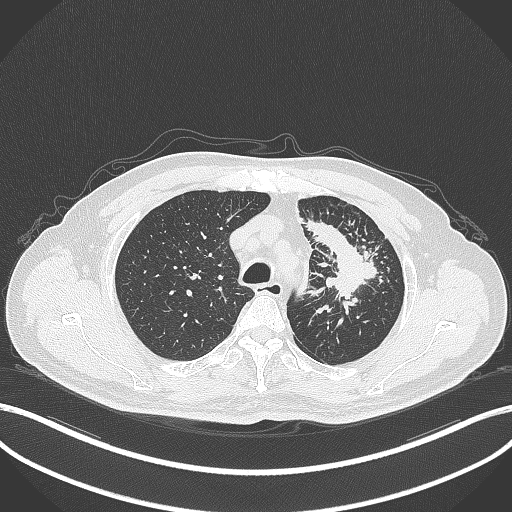
Chest CT, one axial slice. Position 277 of 386 along the scan axis. Reconstruction kernel B70f. 120 kVp. Lung window (W 1500 / L -600 HU). 1 mm slice thickness. 512 × 512 image matrix, field of view 400 × 400 mm. Male patient, age 69 years. From the clinical record (not read from this slice): clinical TNM (as recorded): T2a N2 M0.
Outlined on this slice (bounding box drawn by a radiologist):
- lung tumour (recorded histology: adenocarcinoma): bounding box <303,219,383,305> (left, top, right, bottom; pixels)